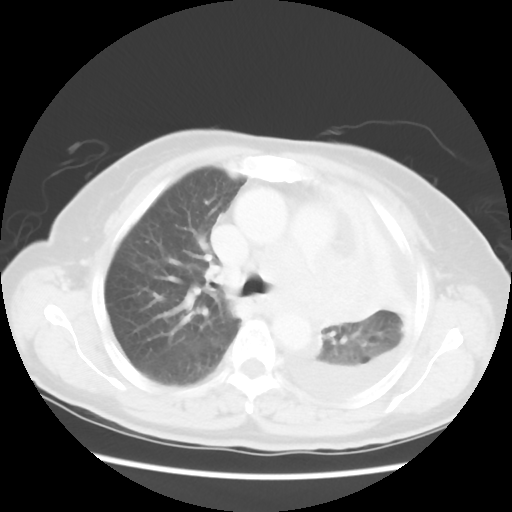
Chest CT, one axial slice; position 36 of 52 along the scan axis; reconstruction kernel STANDARD; 120 kVp; lung window (W 1500 / L -600 HU); 5 mm slice thickness; 512 × 512 image matrix. Female patient, age 72 years. From the clinical record (not read from this slice): clinical TNM (as recorded): T4 N3 M1b; histopathological grade: G3.
Outlined on this slice (rectangle marked by the reading radiologist):
- lung tumour (recorded histology: large cell carcinoma): box from (x=299, y=246) to (x=392, y=338) px